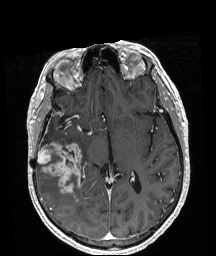
Brain MRI from a brain-tumour surgery series, one axial slice; position 108 of 208 along the scan axis; T1-weighted post-contrast; 1 mm slice thickness; 216 × 256 image matrix, field of view 211 × 250 mm. From the clinical record (not read from this slice): histopathology: Astrocytoma; WHO grade: 4; IDH mutation: yes; tumour location: Right Temporal.
Outlined on this slice (expert manual segmentation):
- tumour: bounding box <38,143,81,193> (left, top, right, bottom; pixels)